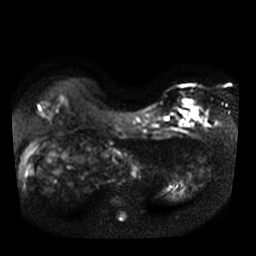
Breast MRI, one axial slice. Diffusion-weighted series; image 2 of 4 stored at this slice position (different b-values; order by instance number). 3 T. 5 mm slice thickness. 256 × 256 image matrix, field of view 320 × 320 mm. Female patient.
Annotated regions visible in this slice (expert manual segmentation):
- tumour on diffusion-weighted imaging: bounding box (x1, y1, x2, y2) in pixels: (185, 100, 198, 119)